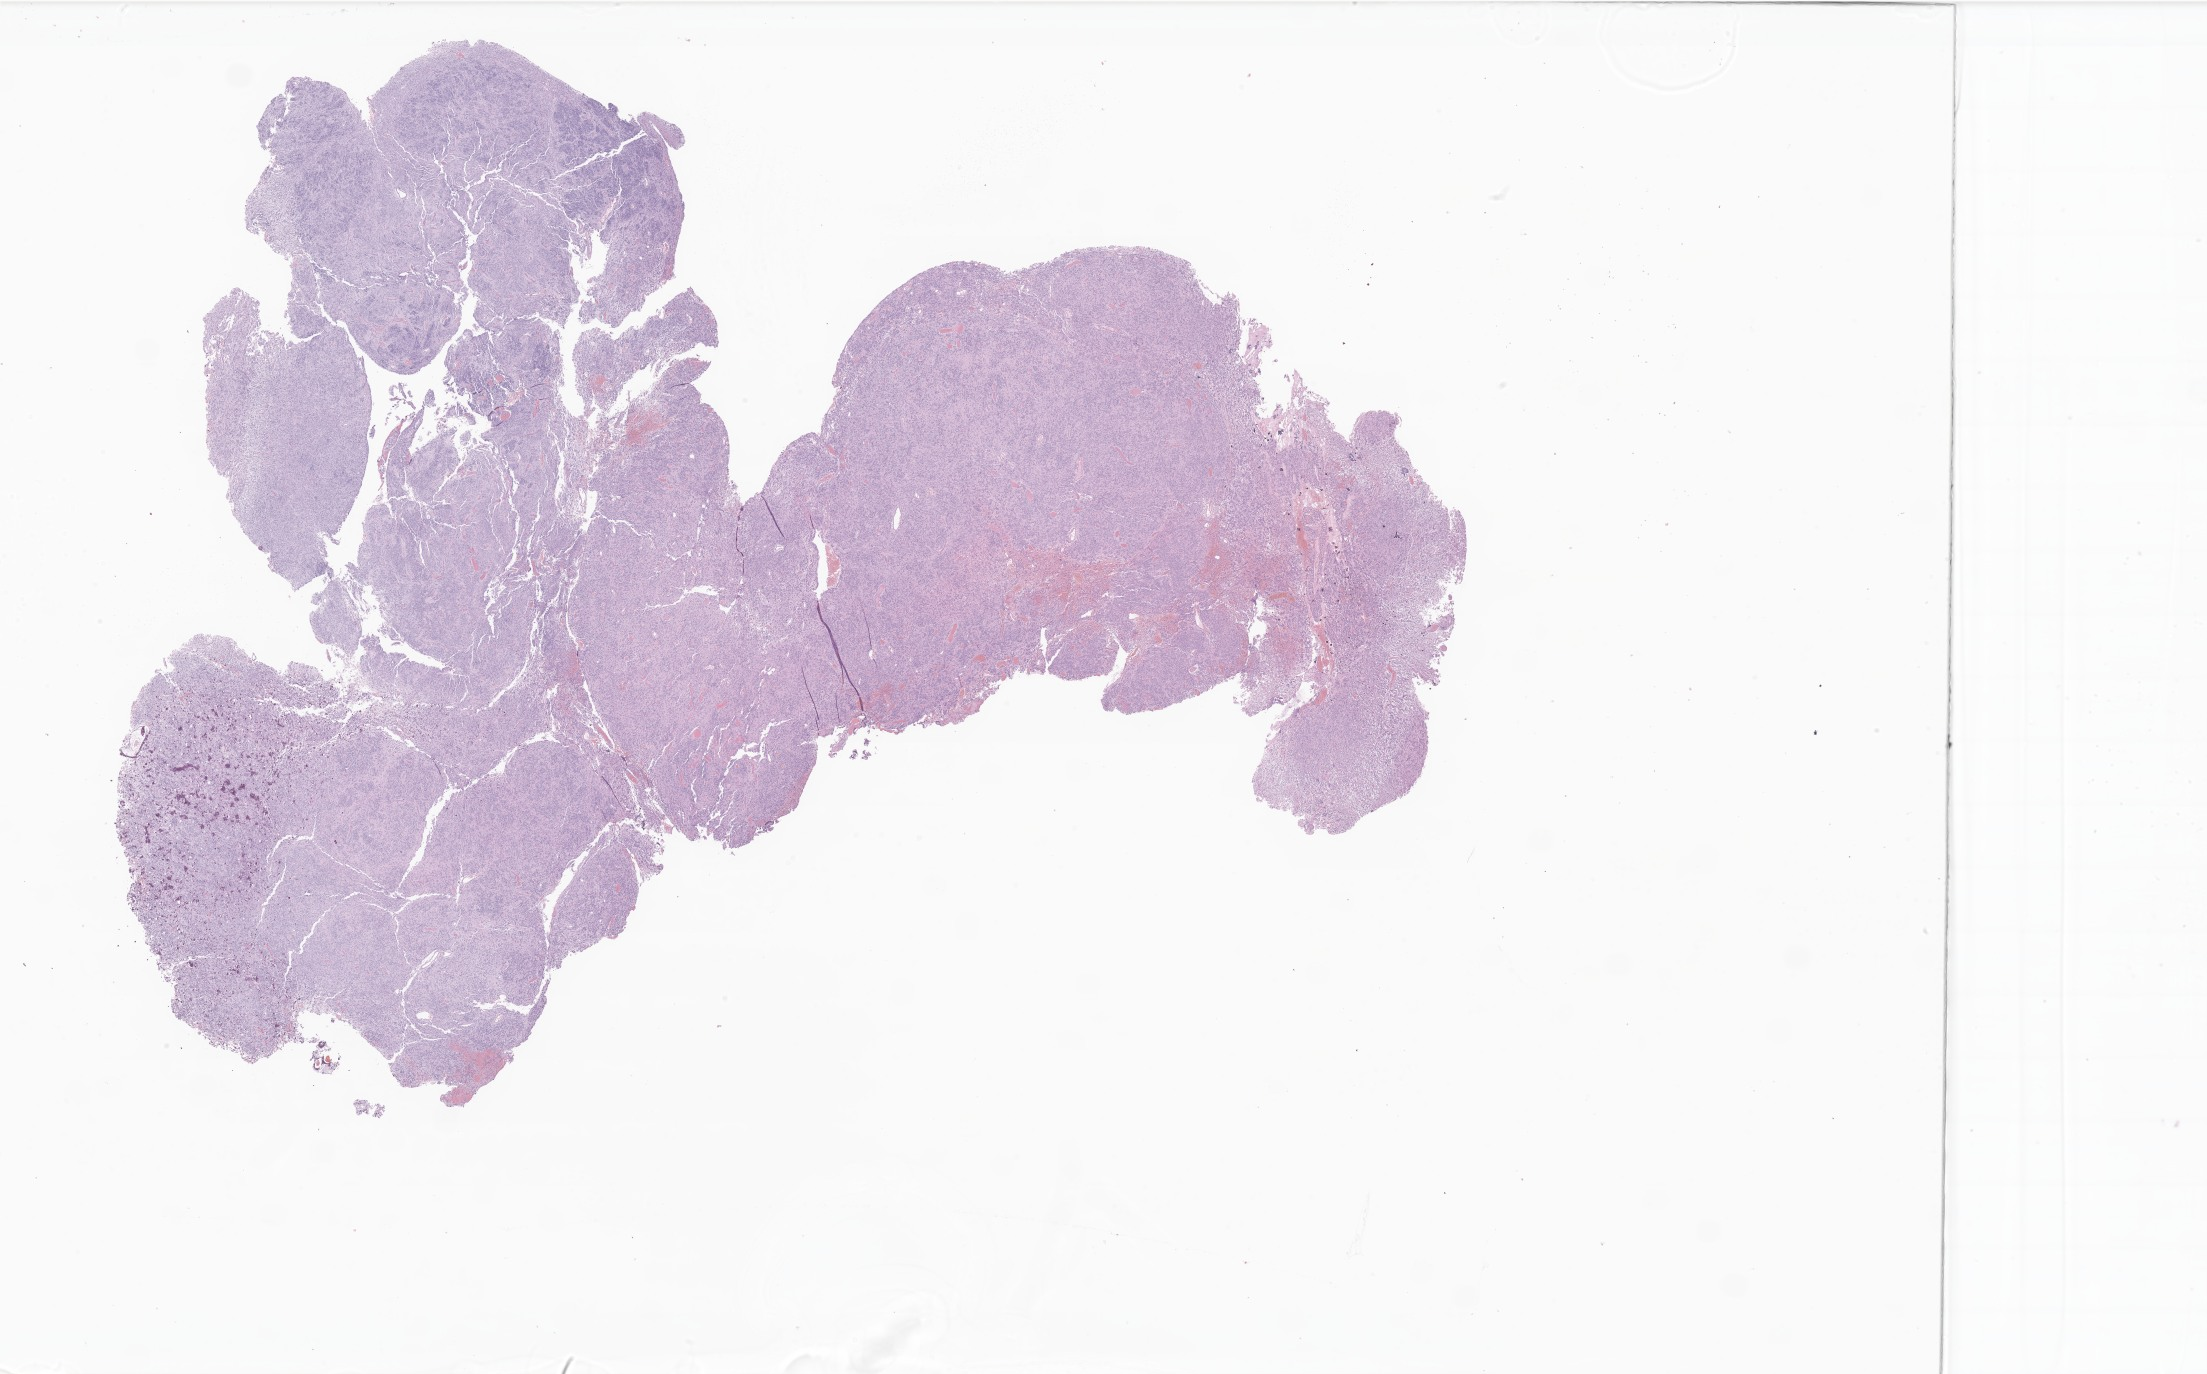
Digitized hematoxylin and eosin (H&E)-stained section of tumor tissue from the frontal lobe, a low-resolution overview of the entire scanned area, about 37.2 x 23.2 mm; formalin-fixed, paraffin-embedded (FFPE) tissue. Patient: female, age 41 months (3 years 5 months).
* diagnosis (ICD-O-3 morphology term): Ependymoma, NOS